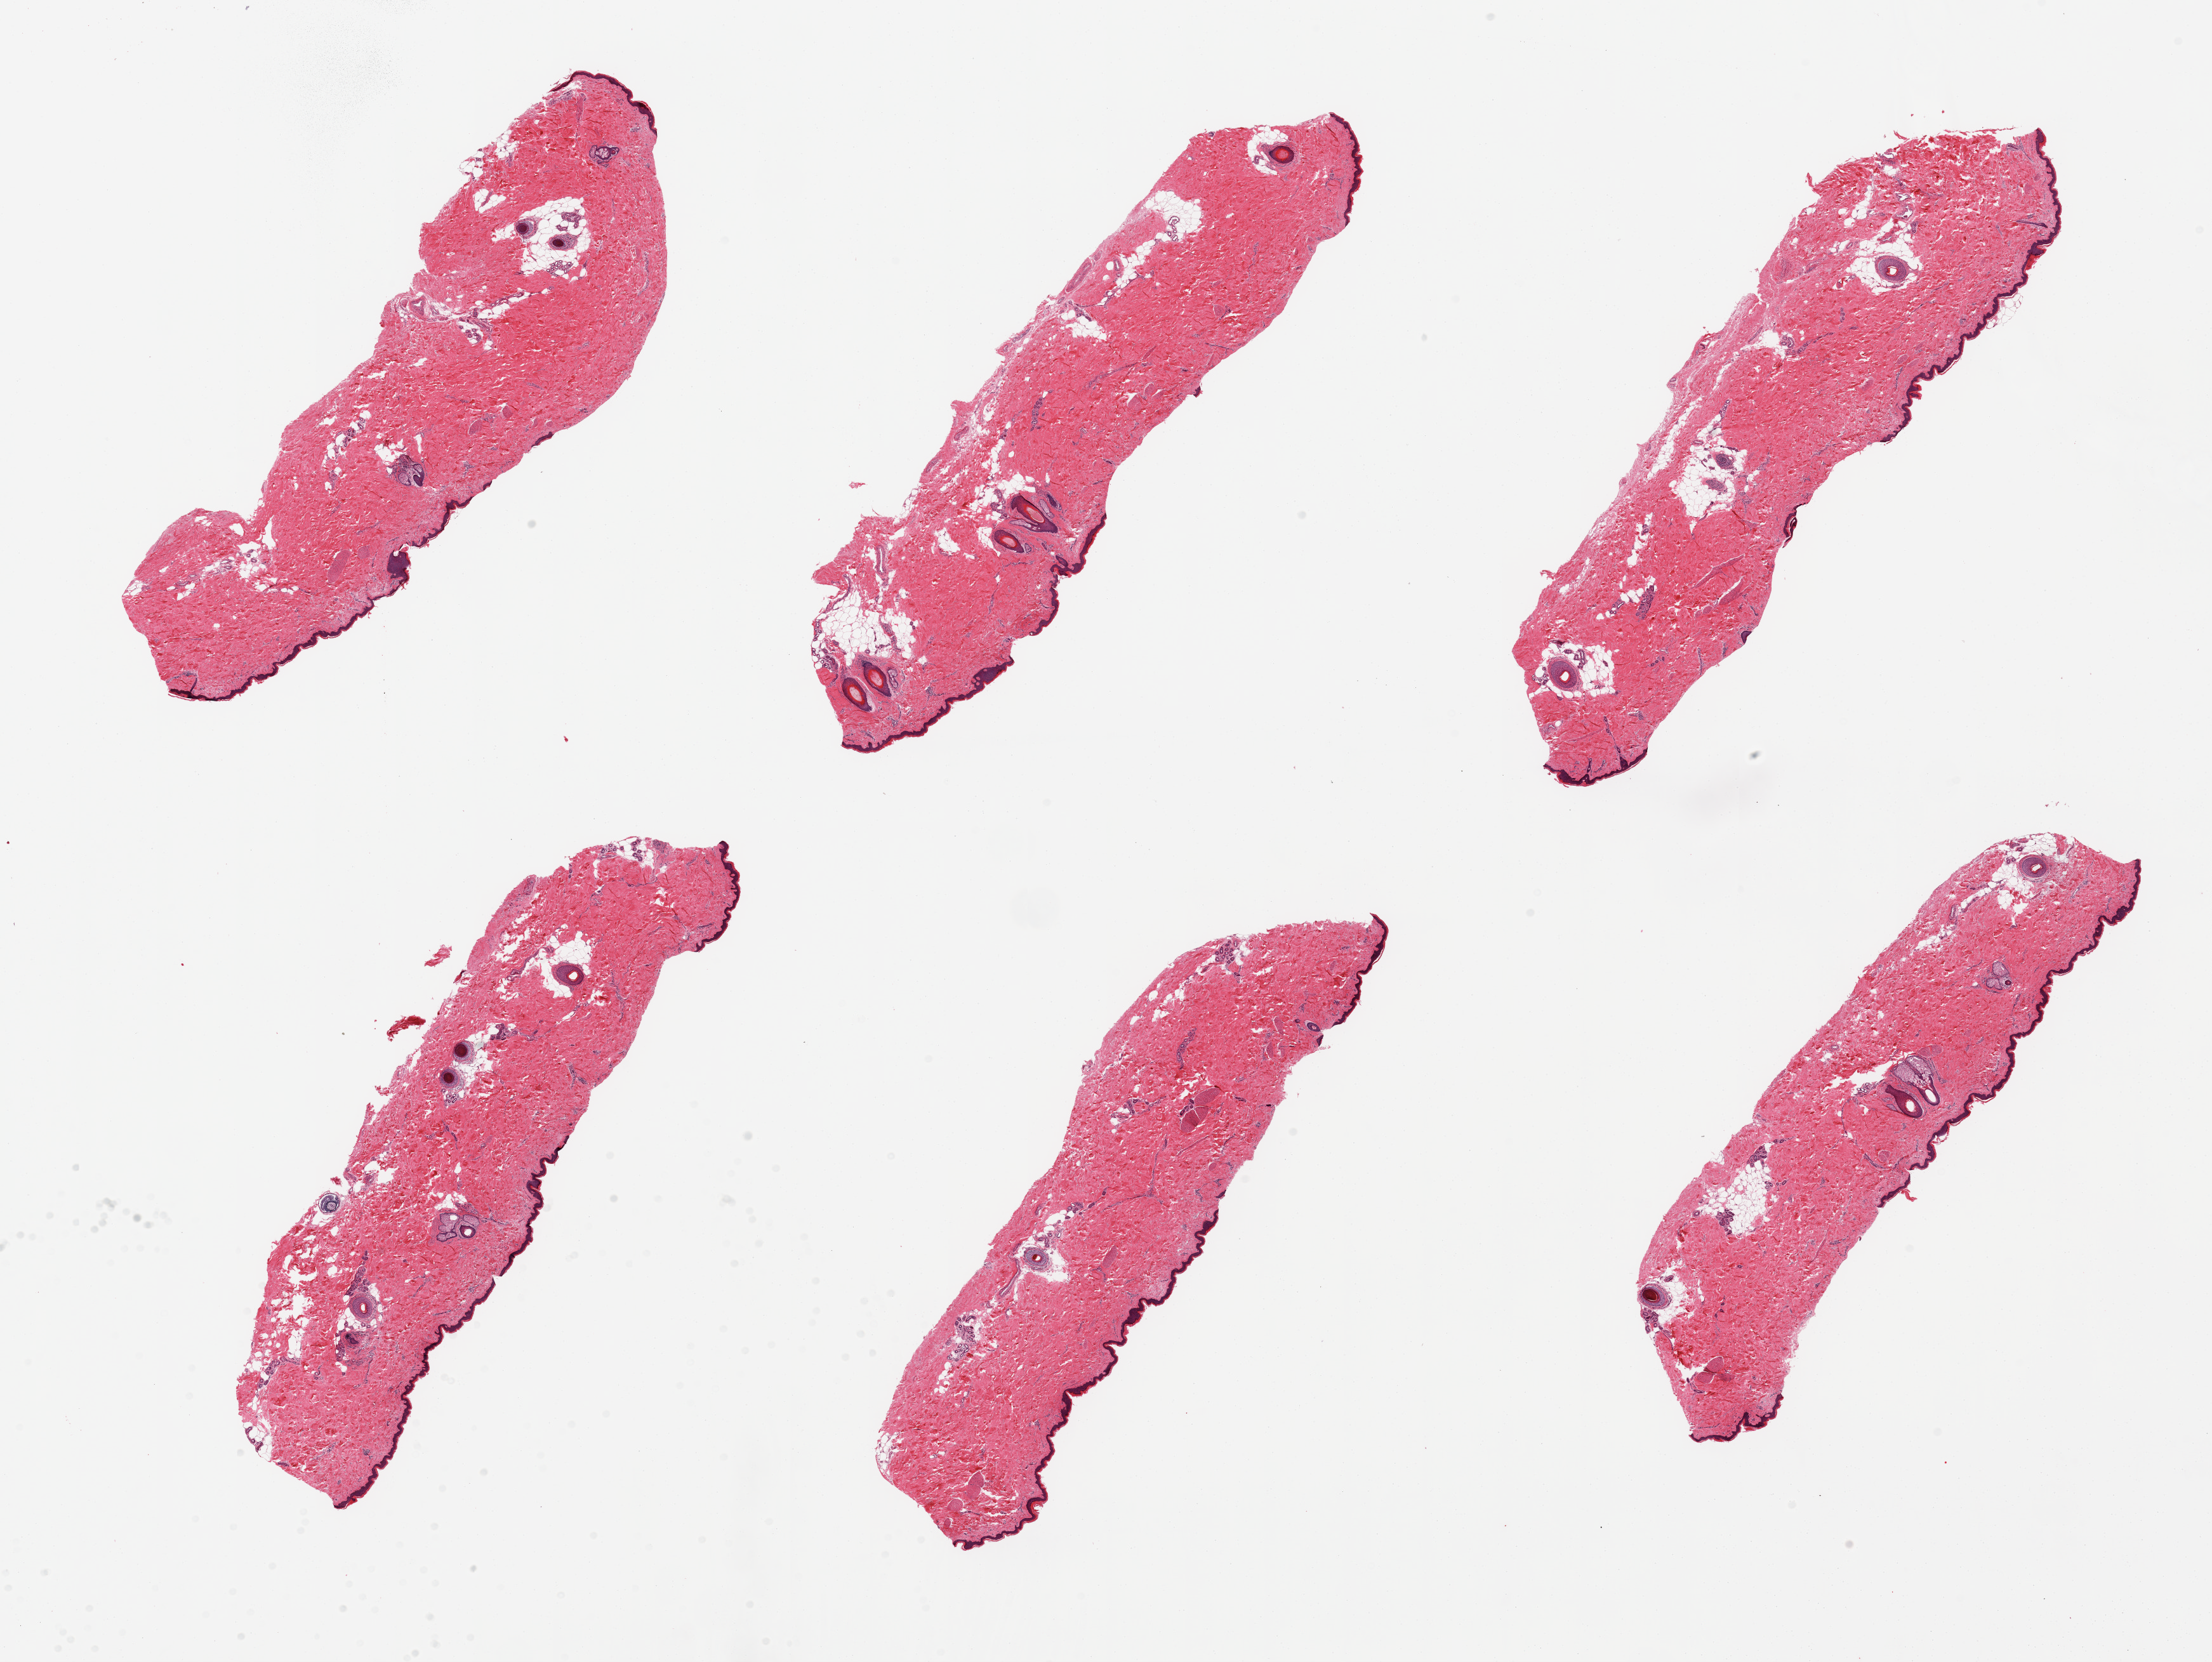
Whole-slide image, H&E stain, shown as a low-resolution overview of the whole scanned area (about 27.6 x 20.7 mm, acquisition: 20x scan); PAXgene-fixed, paraffin-embedded tissue; target tissue: skin of lower leg; donor tissue sample. Male donor.
Review note (as recorded): 6 pieces, minmal dermal fat, squamous epithelium is ~50-60microns.